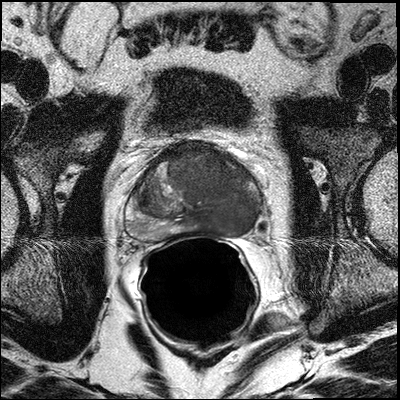
Prostate MRI examination; 3 images, each a single mid-volume slice chosen by position (not for content). Treatment context recorded for this patient: No surgery. Patient has received definitive RT, casodex and lupron.
Image 1: axial T2-weighted image, series "T2W_TSE_AX", slice 15 of 28, 3 mm slice thickness.
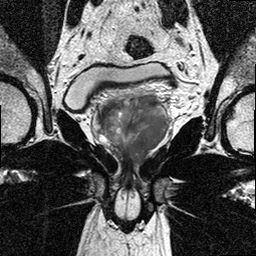
Image 2: T2-weighted coronal slice, series "T2W_TSE_COR", slice 13 of 24, 3 mm slice thickness.
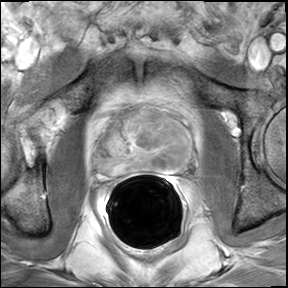
Image 3: DCE (dynamic gadolinium-enhanced) axial slice, series "AX BLISS_GAD", slice 15 of 28, dynamic phase 4 of 7.
MRI report (verbatim):
Prostate measures 5.8 x 3.7 x 4.5 cm (estimated volume: 50 cc). There is a large mass seen predominantly on the left side involving the peripheral zone of the base, midthird and apex as well the central gland of the left (approx 50% of the gland are involved). The mass crosses the midline several times especially in midthird and apex and involves right peripheral zone and right central gland. The mass abuts the urethra in the apex, with signs of infiltration of the urethra. (series 501 slice location 15 image 6). Imaging findings are suggestive for extraprostatic disease at 1) the apex (median) , 2) at the left internal sphincter, with beginning involvement of the muscle, 3) anteriorly beyond the fibromuscular band at the apex and midthird and 4) at the level of midthird and apex the tumor (median and paramedian left) abuts the Denonvilliers fascia (series 501/slice location 21/ image 8). No evidence for involvement of the neurovascular bundle on either side. No evidence for seminal vesicles infiltration. No evidence of involvement of bladder neck. No suspiciously enlarged obturator and iliac lymph nodes.

Prostate biopsy pathology (as recorded):
specimen is submitted entirely in six cassettes as follows: 1-right PZ, 2-right PZ/TZ, 3-right apex, 4-left PZ, 5-left PZ/TZ, 6-left apex. Final Diagnosis 1. RIGHT PZ: BENIGN PROSTATIC TISSUE, NO TUMOR IDENTIFIED. NOTE: IMMUNOHISTOCHEMISTRY STUDIES PERFORMED ON PARAFFIN EMBEDDED TISSUE BLOCK FOR PIN4 (RACEMASE/K309 AND P63) DID NOT REVEAL A STAINING PATTERN DIAGNOSTIC OF INVASIVE CARCINOMA. 2. RIGHT PZ/TZ: BENIGN PROSTATIC TISSUE WITH CHRONIC INFLAMMATION, NO TUMOR IDENTIFIED. 3. RIGHT APEX: BENIGN PROSTATIC TISSUE, NO TUMOR IDENTIFIED. 4. LEFT PZ: PROSTATIC ADENOCARCINOMA, GLEASON SCORE 4+3=7/10, INVOLVING TWO CORES, ABOUT 60% OF THE TISSUE REPRESENTED. PERINEURAL INVASION IS PRESENT. 5. LEFT PZ/TZ: PROSTATIC ADENOCARCINOMA, GLEASON SCORE 4+3=7/10, INVOLVING TWO CORES, ABOUT 70% OF THE TISSUE REPRESENTED. PERINEURAL INVASION IS PRESENT. 6. LEFT APEX: PROSTATIC ADENOCARCINOMA, GLEASON SCORE 4+3=7/10, INVOLVING TWO CORES, ABOUT 70% OF THE TISSUE REPRESENTED. PERINEURAL INVASION IS PRESENT.